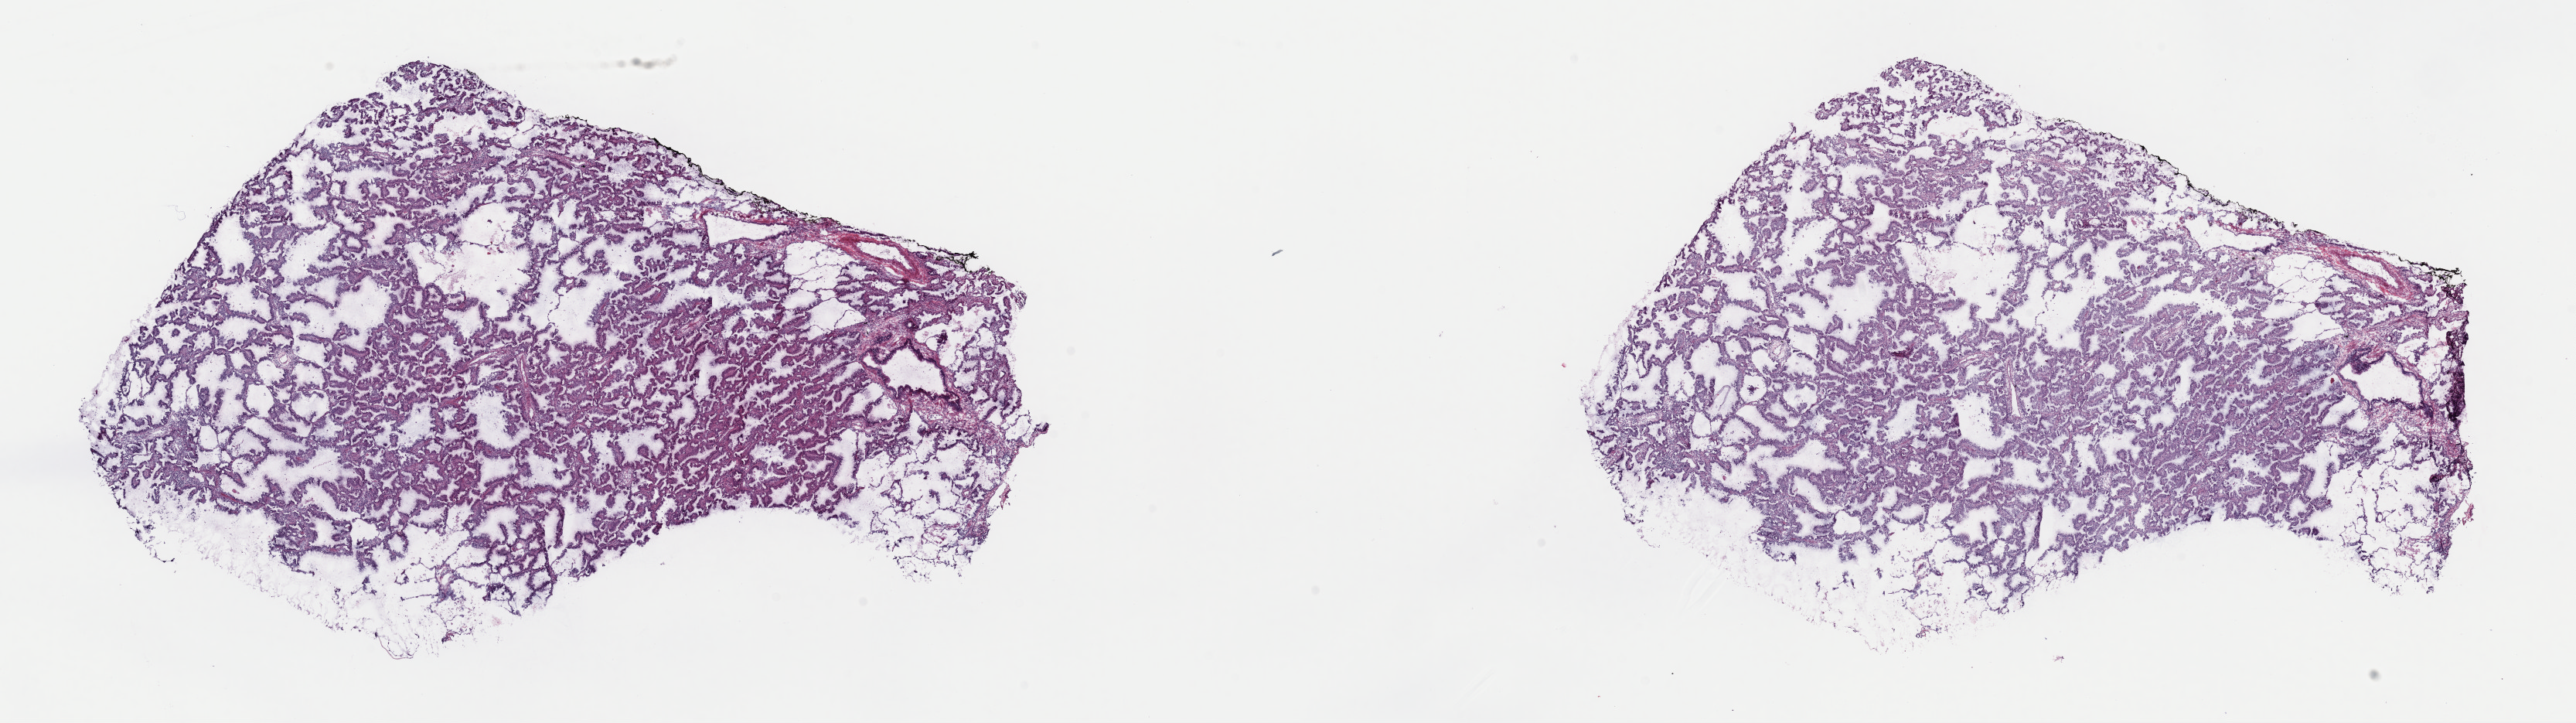
Digitized Hematoxylin and eosin (H&E) stained tissue section (whole slide) — shown as a low-resolution overview of the whole scanned area (about 26.3 x 7.4 mm, from a 40x scan). Frozen section. Sample: primary tumour, lung. Patient: male, age at initial diagnosis 64 years.
Pathologic diagnosis: Mucinous adenocarcinoma (lower lobe, lung).